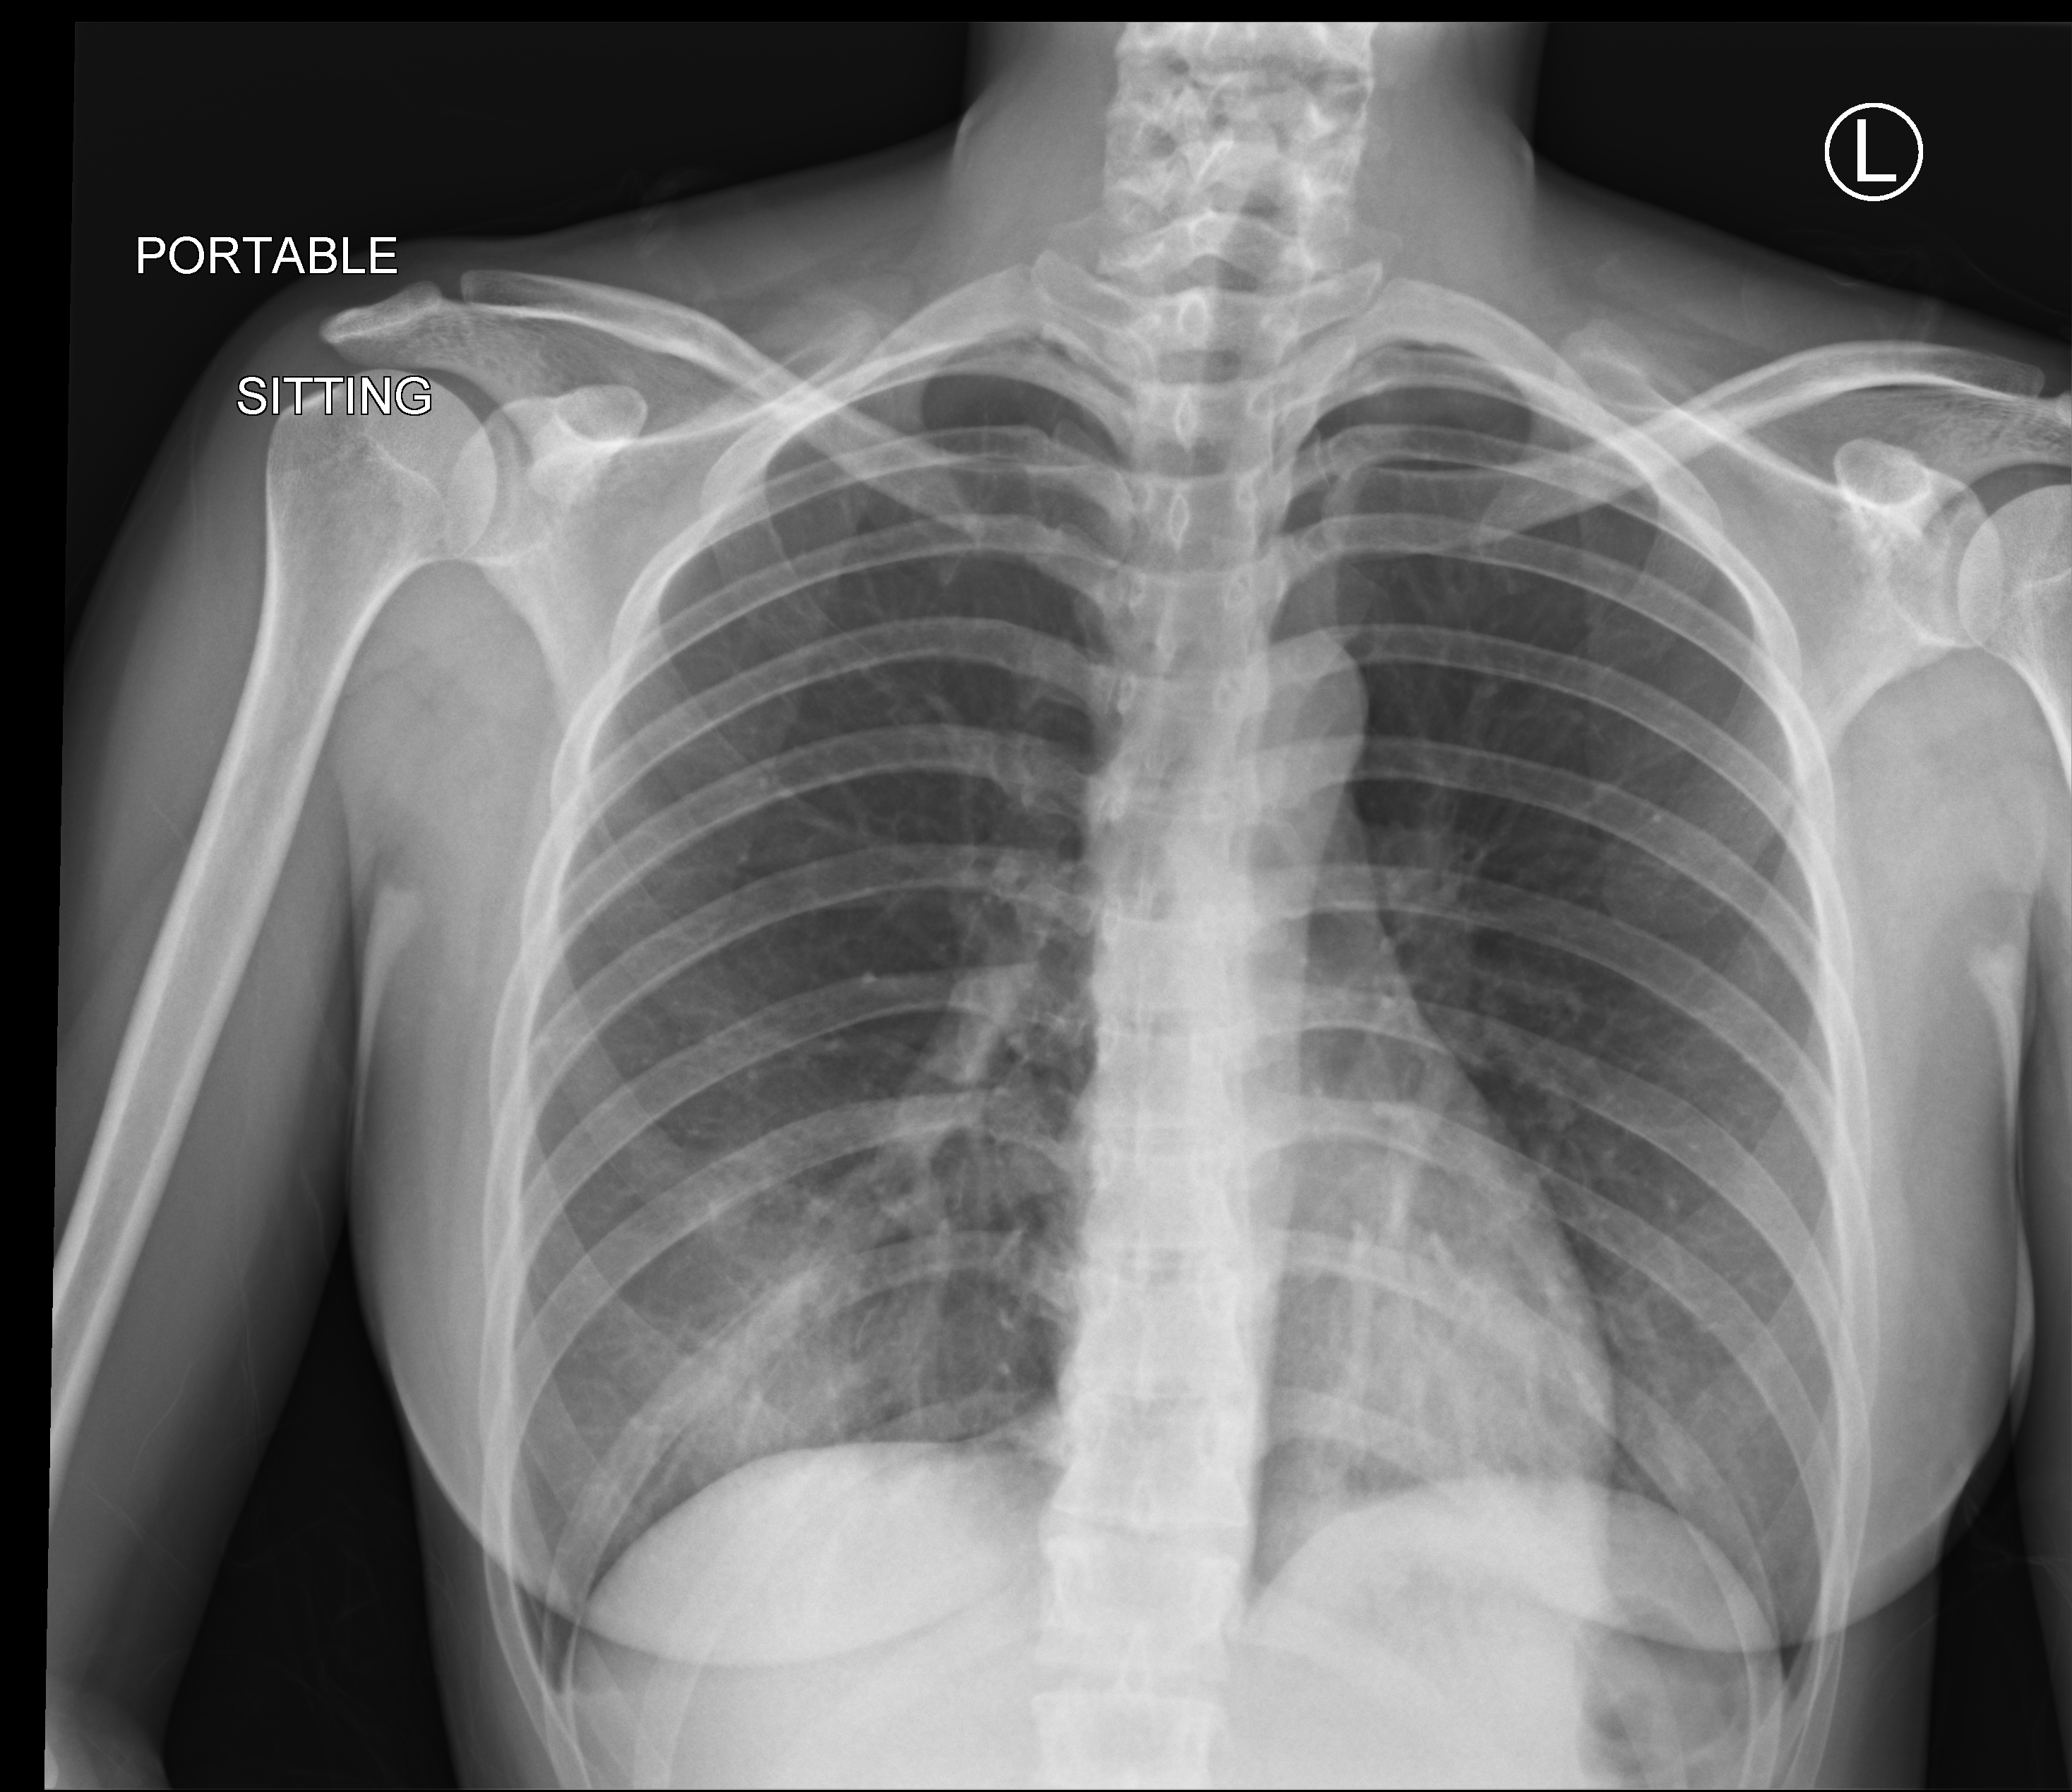
Chest X-ray (portable), anteroposterior (AP) projection. Patient hospitalised with COVID-19; female, aged 18–59 years.
From the hospital-stay record, not from the radiograph (when in the stay this image was taken is not recorded): admitted to intensive care during this hospital stay: no; hypertension (admission record): no; other chronic lung disease (admission record): no.